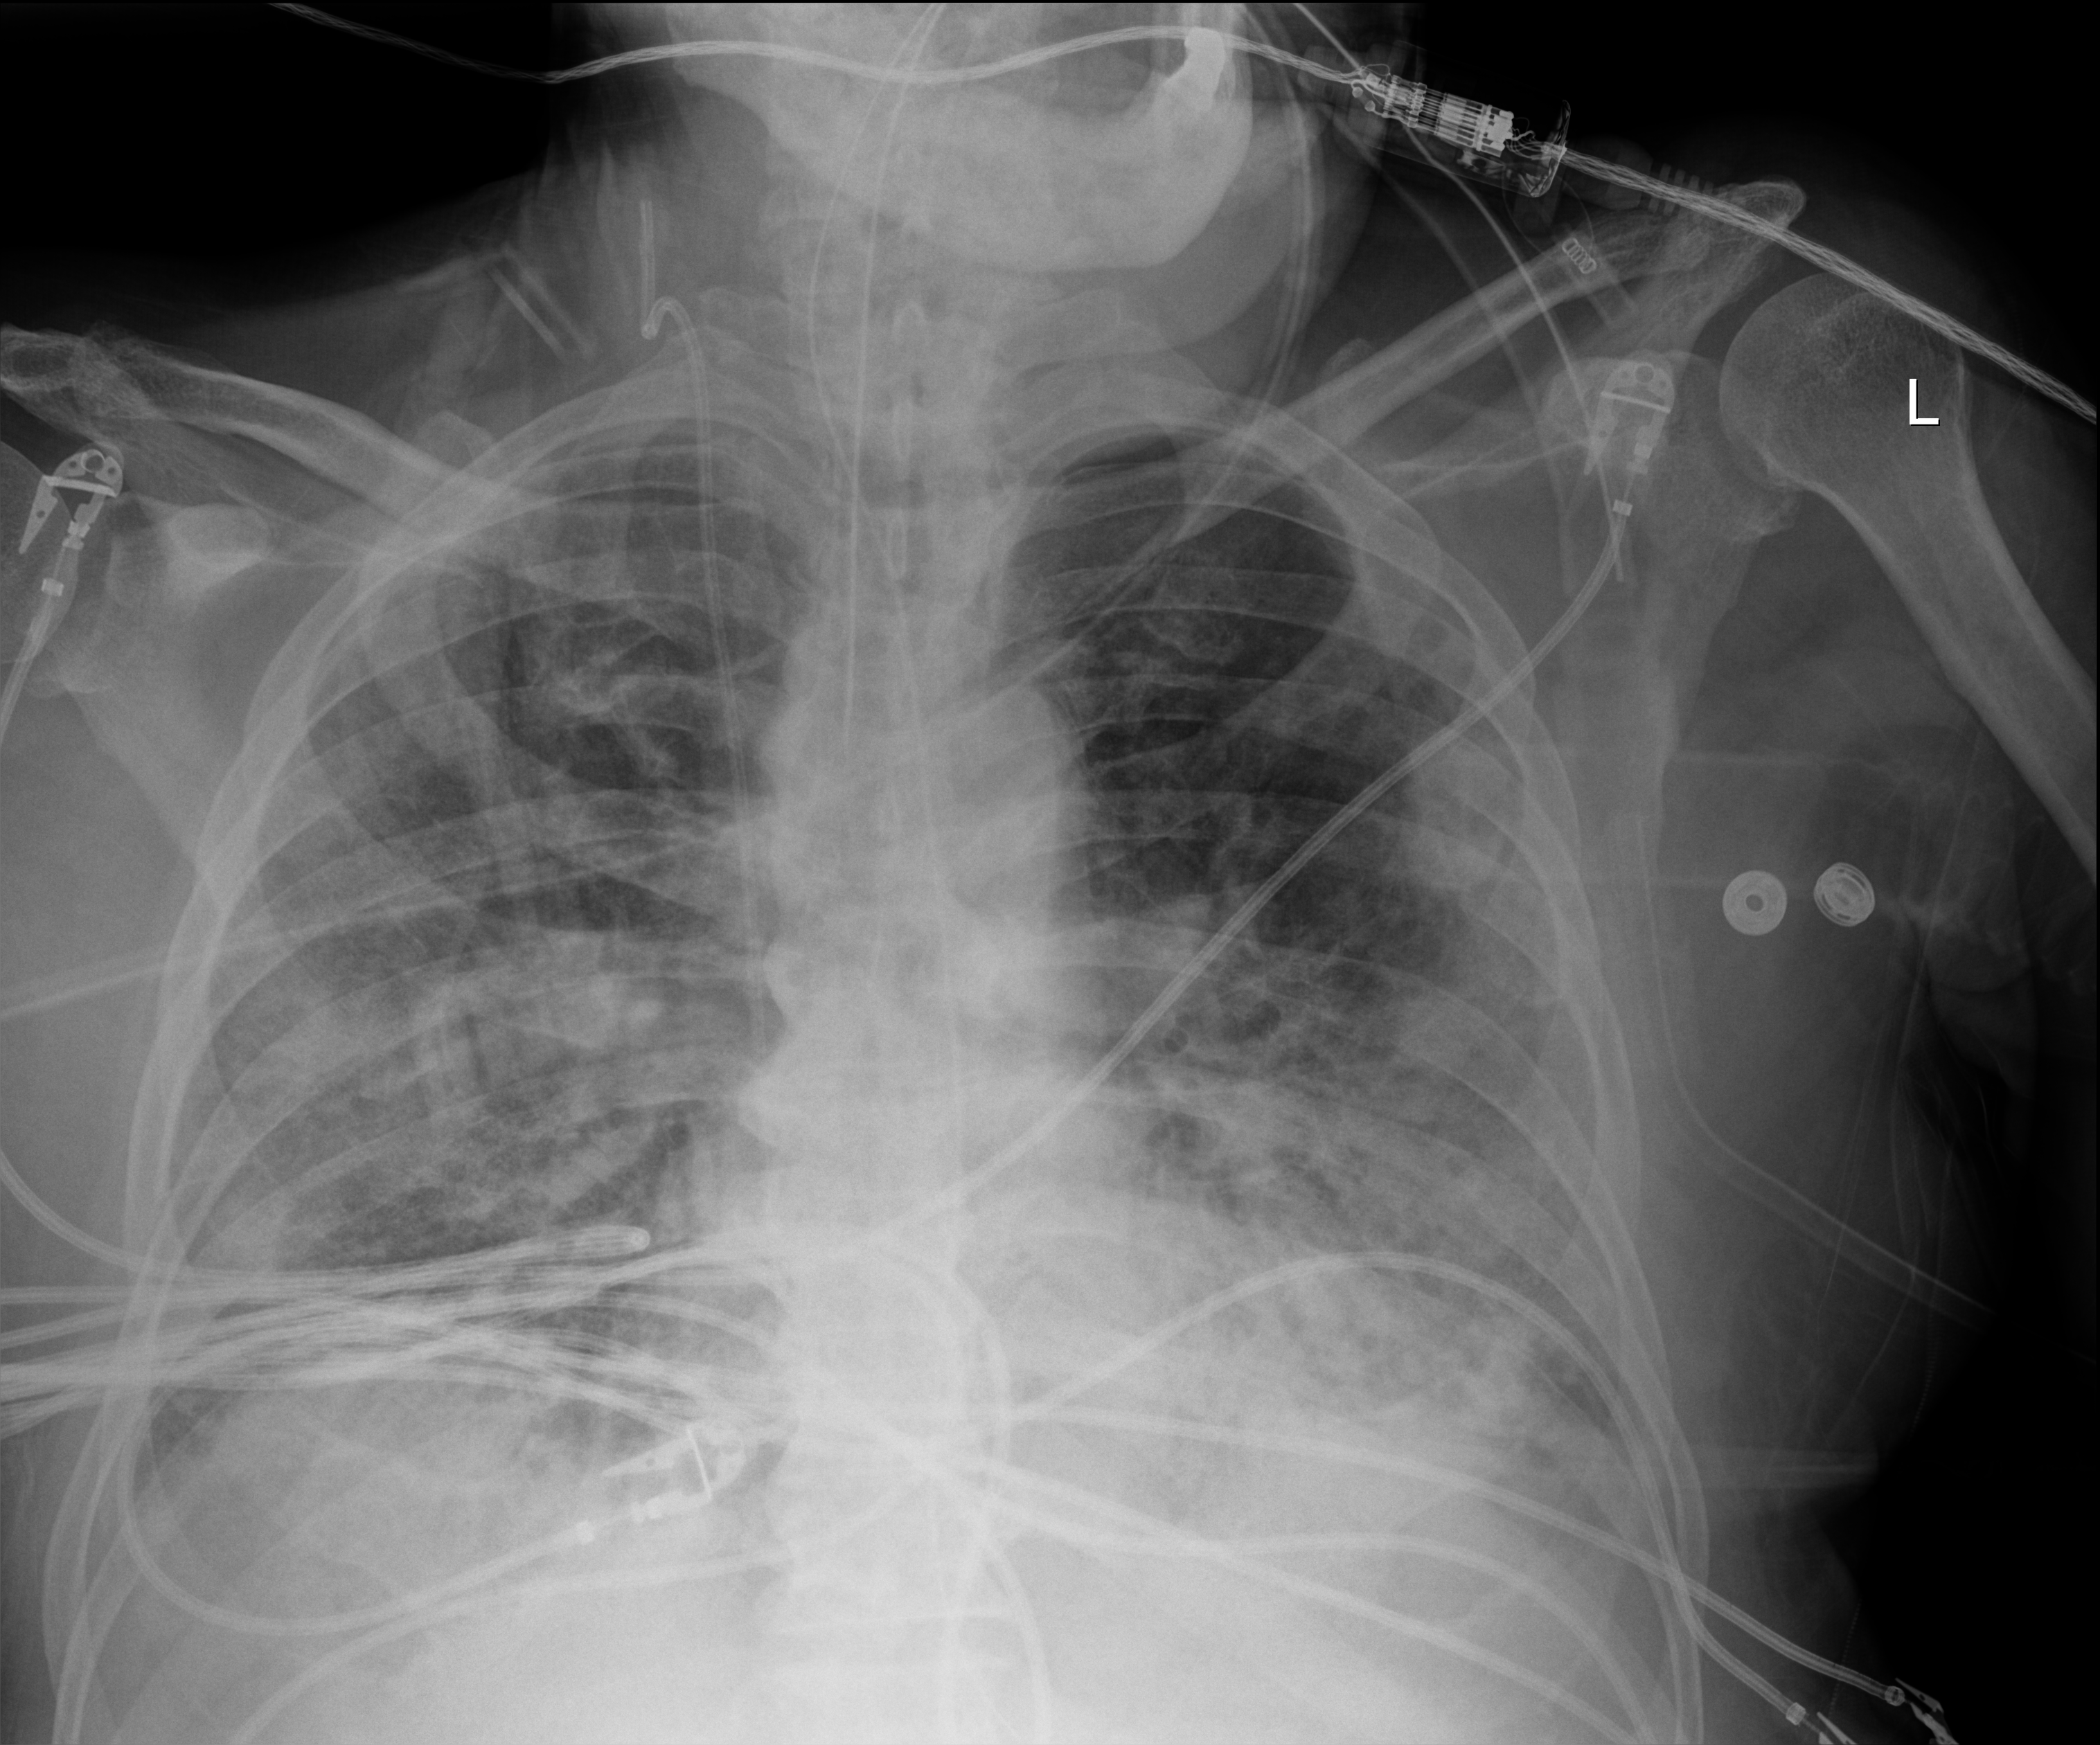
Chest X-ray (portable). Male patient hospitalised with COVID-19, age 75–90 years.
Admission-level facts for this patient (not findings on this image; timing relative to this image not recorded):
- chronic kidney disease (admission record): no